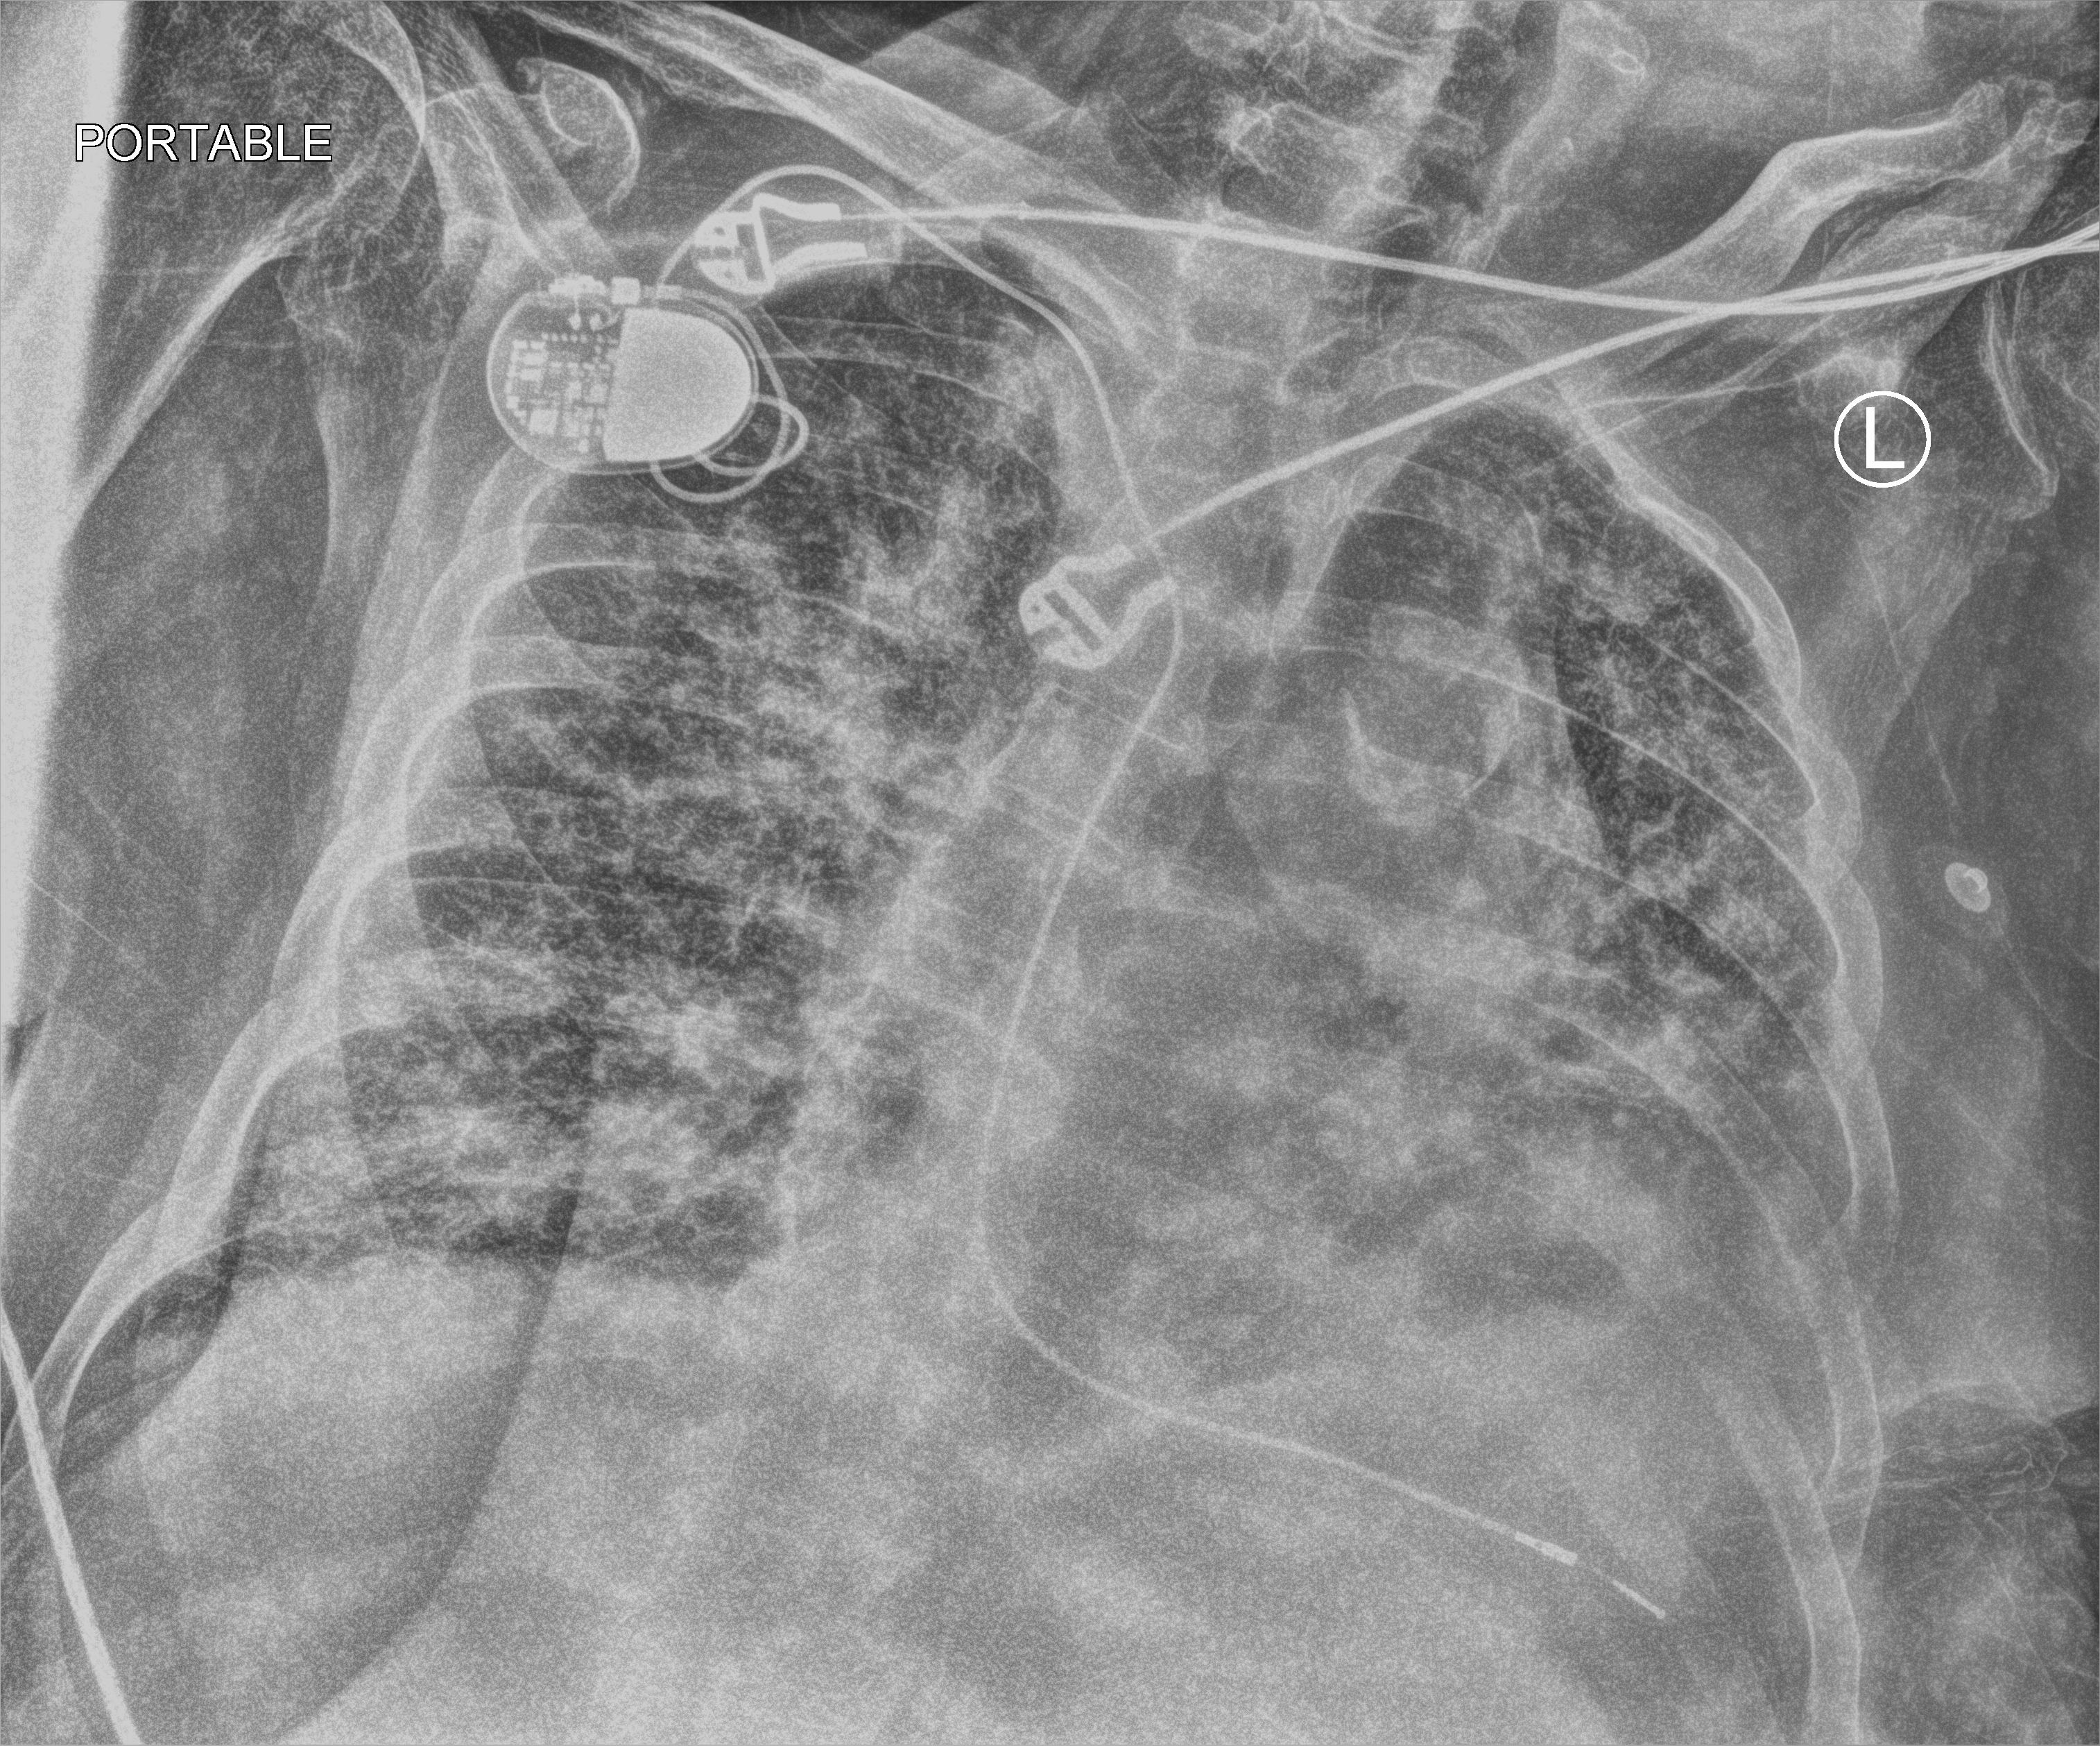
Portable chest radiograph, anteroposterior (AP) projection. Patient hospitalised with COVID-19; male, aged 75–90 years.
Admission-level facts for this patient (not findings on this image; timing relative to this image not recorded):
- admitted to intensive care during this hospital stay: no